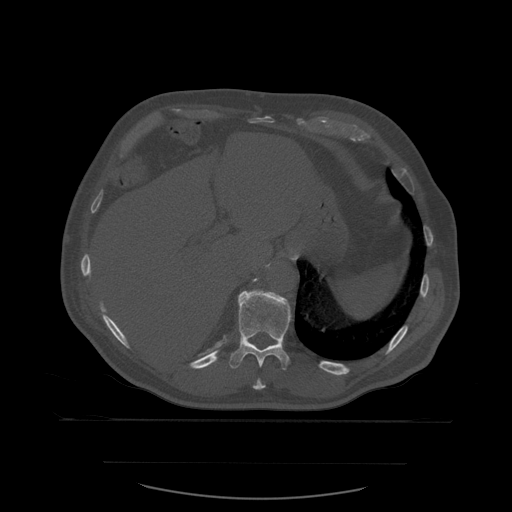
CT including the spine, one axial slice; slice 296 of 590 in the series (ordered by position); bone window (W 1800 / L 400 HU); 1.25 mm slice thickness; 512 × 512 image matrix, field of view 479 × 479 mm. Patient age 71 years. Case-level facts recorded for this patient, not image findings: primary cancer: lung; vertebrae with lytic lesions (as recorded): T1, T2, L5, S1.
Outlined on this slice (semi-automatic segmentation, software-assisted and operator-edited):
- T10 vertebra: box from (x=253, y=379) to (x=266, y=390) px
- T11 vertebra: (x=229, y=290)–(x=292, y=390)